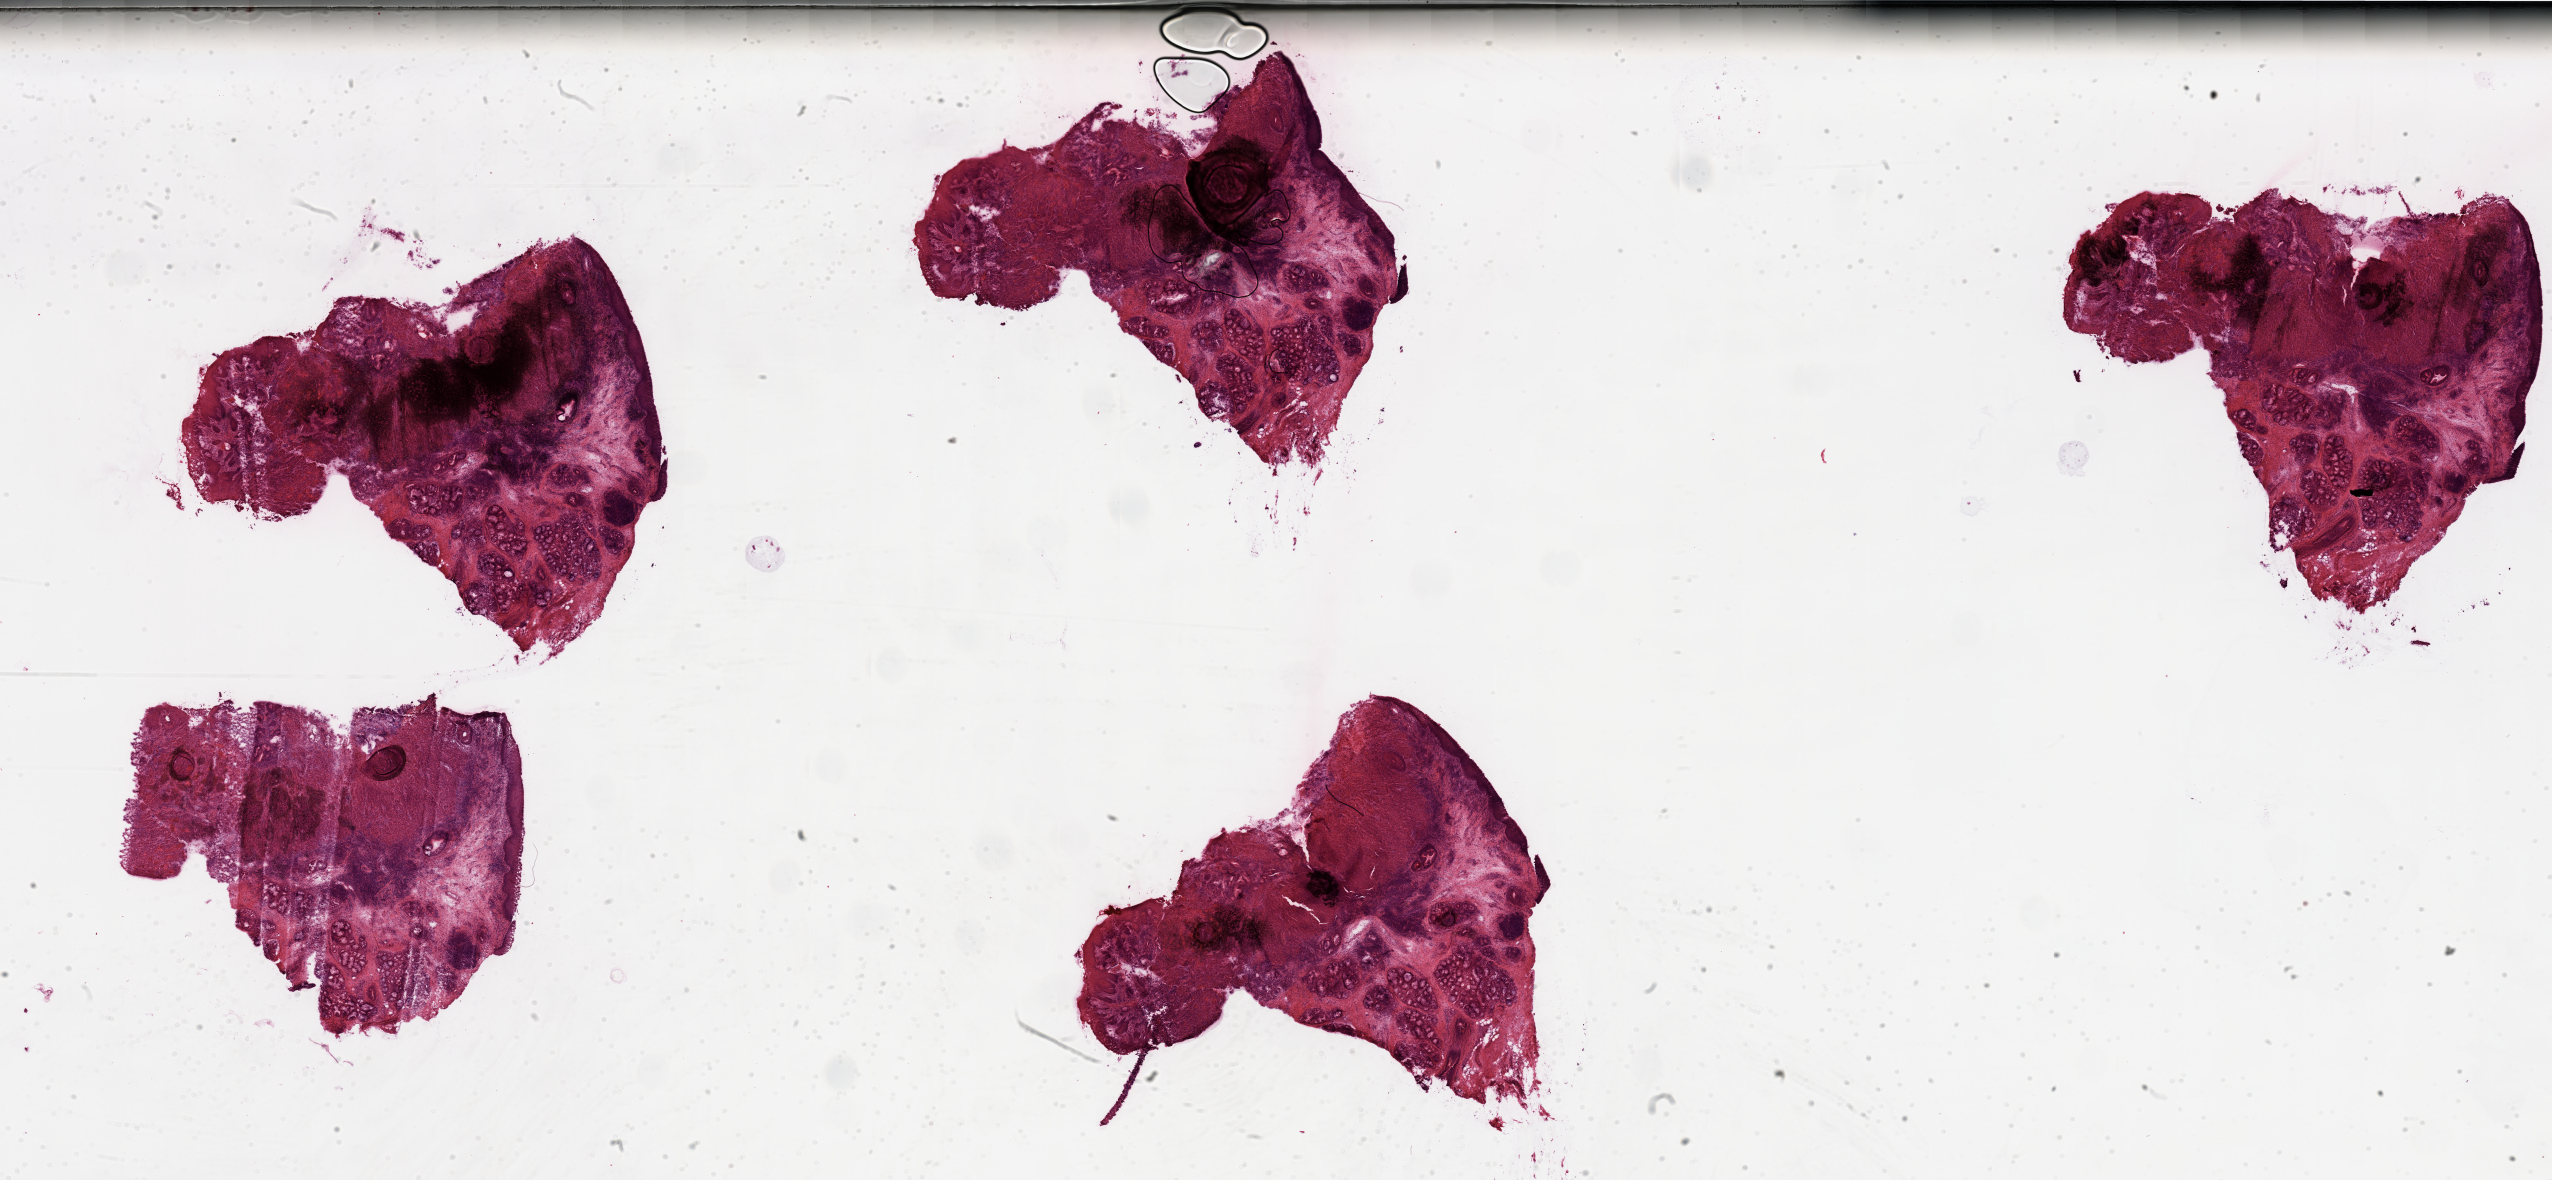
Whole-slide histology image, H&E, shown as a low-resolution overview of the whole scanned area (about 40.4 x 18.7 mm), head and neck, tissue type not recorded. Patient: male, age 50 years.
Patient diagnosis: Squamous cell carcinoma, NOS (larynx, NOS).